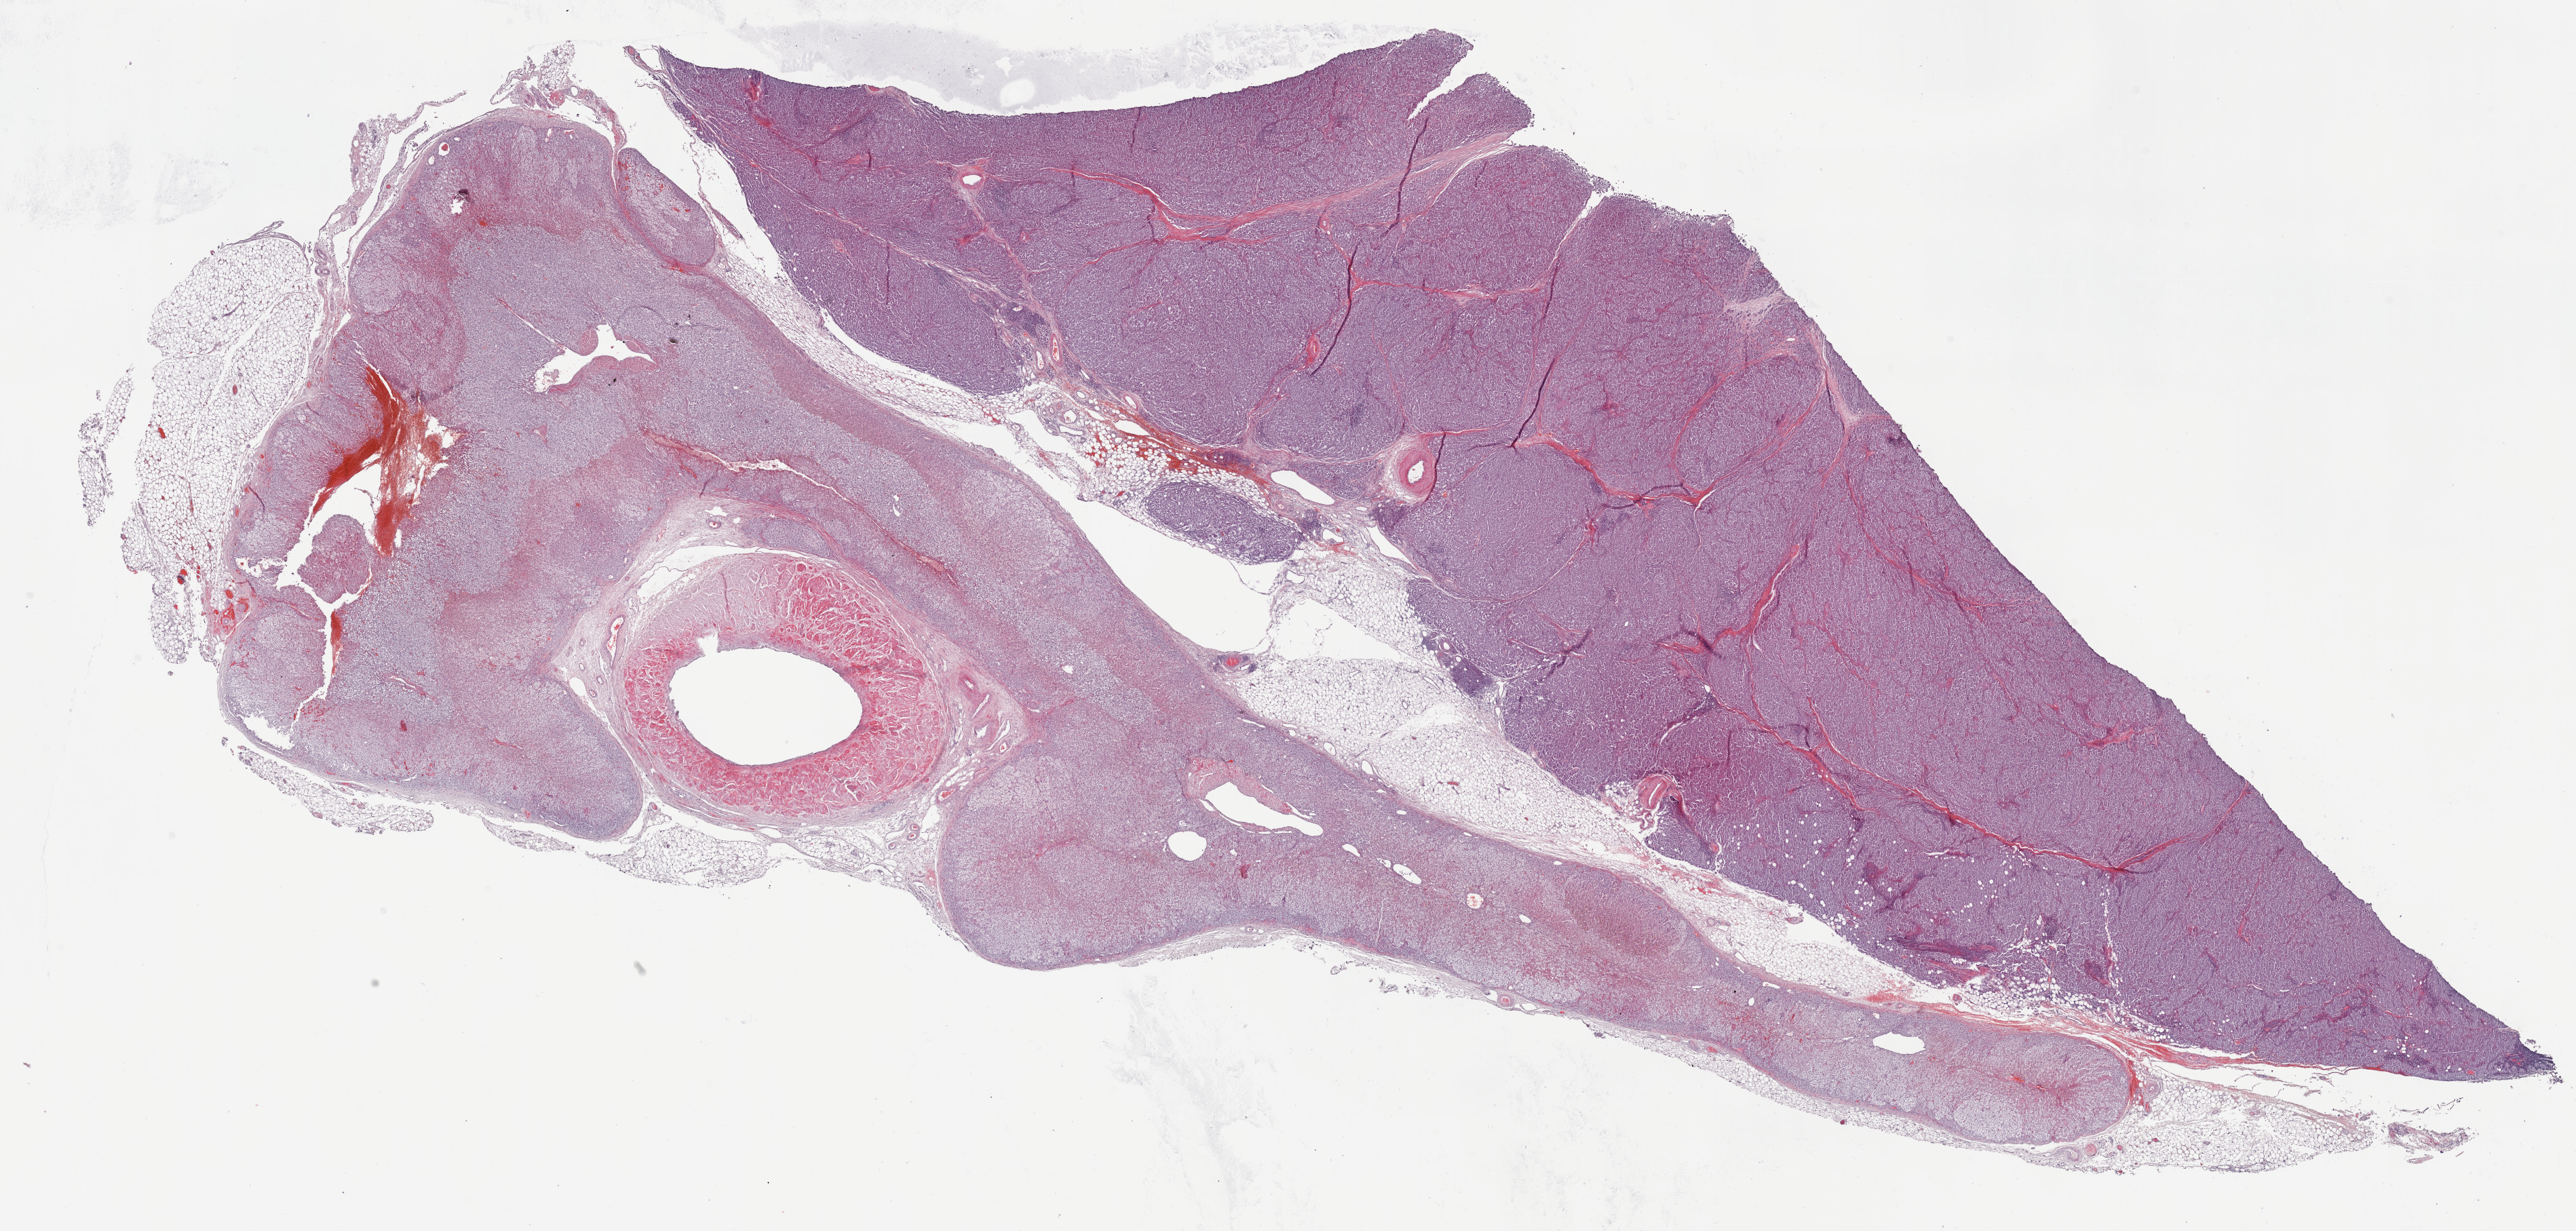
Digitized H&E tissue section (whole slide), whole scanned area (about 30.7 x 14.7 mm) shown as a low-resolution overview; formalin-fixed paraffin-embedded (FFPE) diagnostic section; skin, primary tumour sample. Male patient; age at initial diagnosis 57 years.
- pathologic diagnosis: Malignant melanoma, NOS